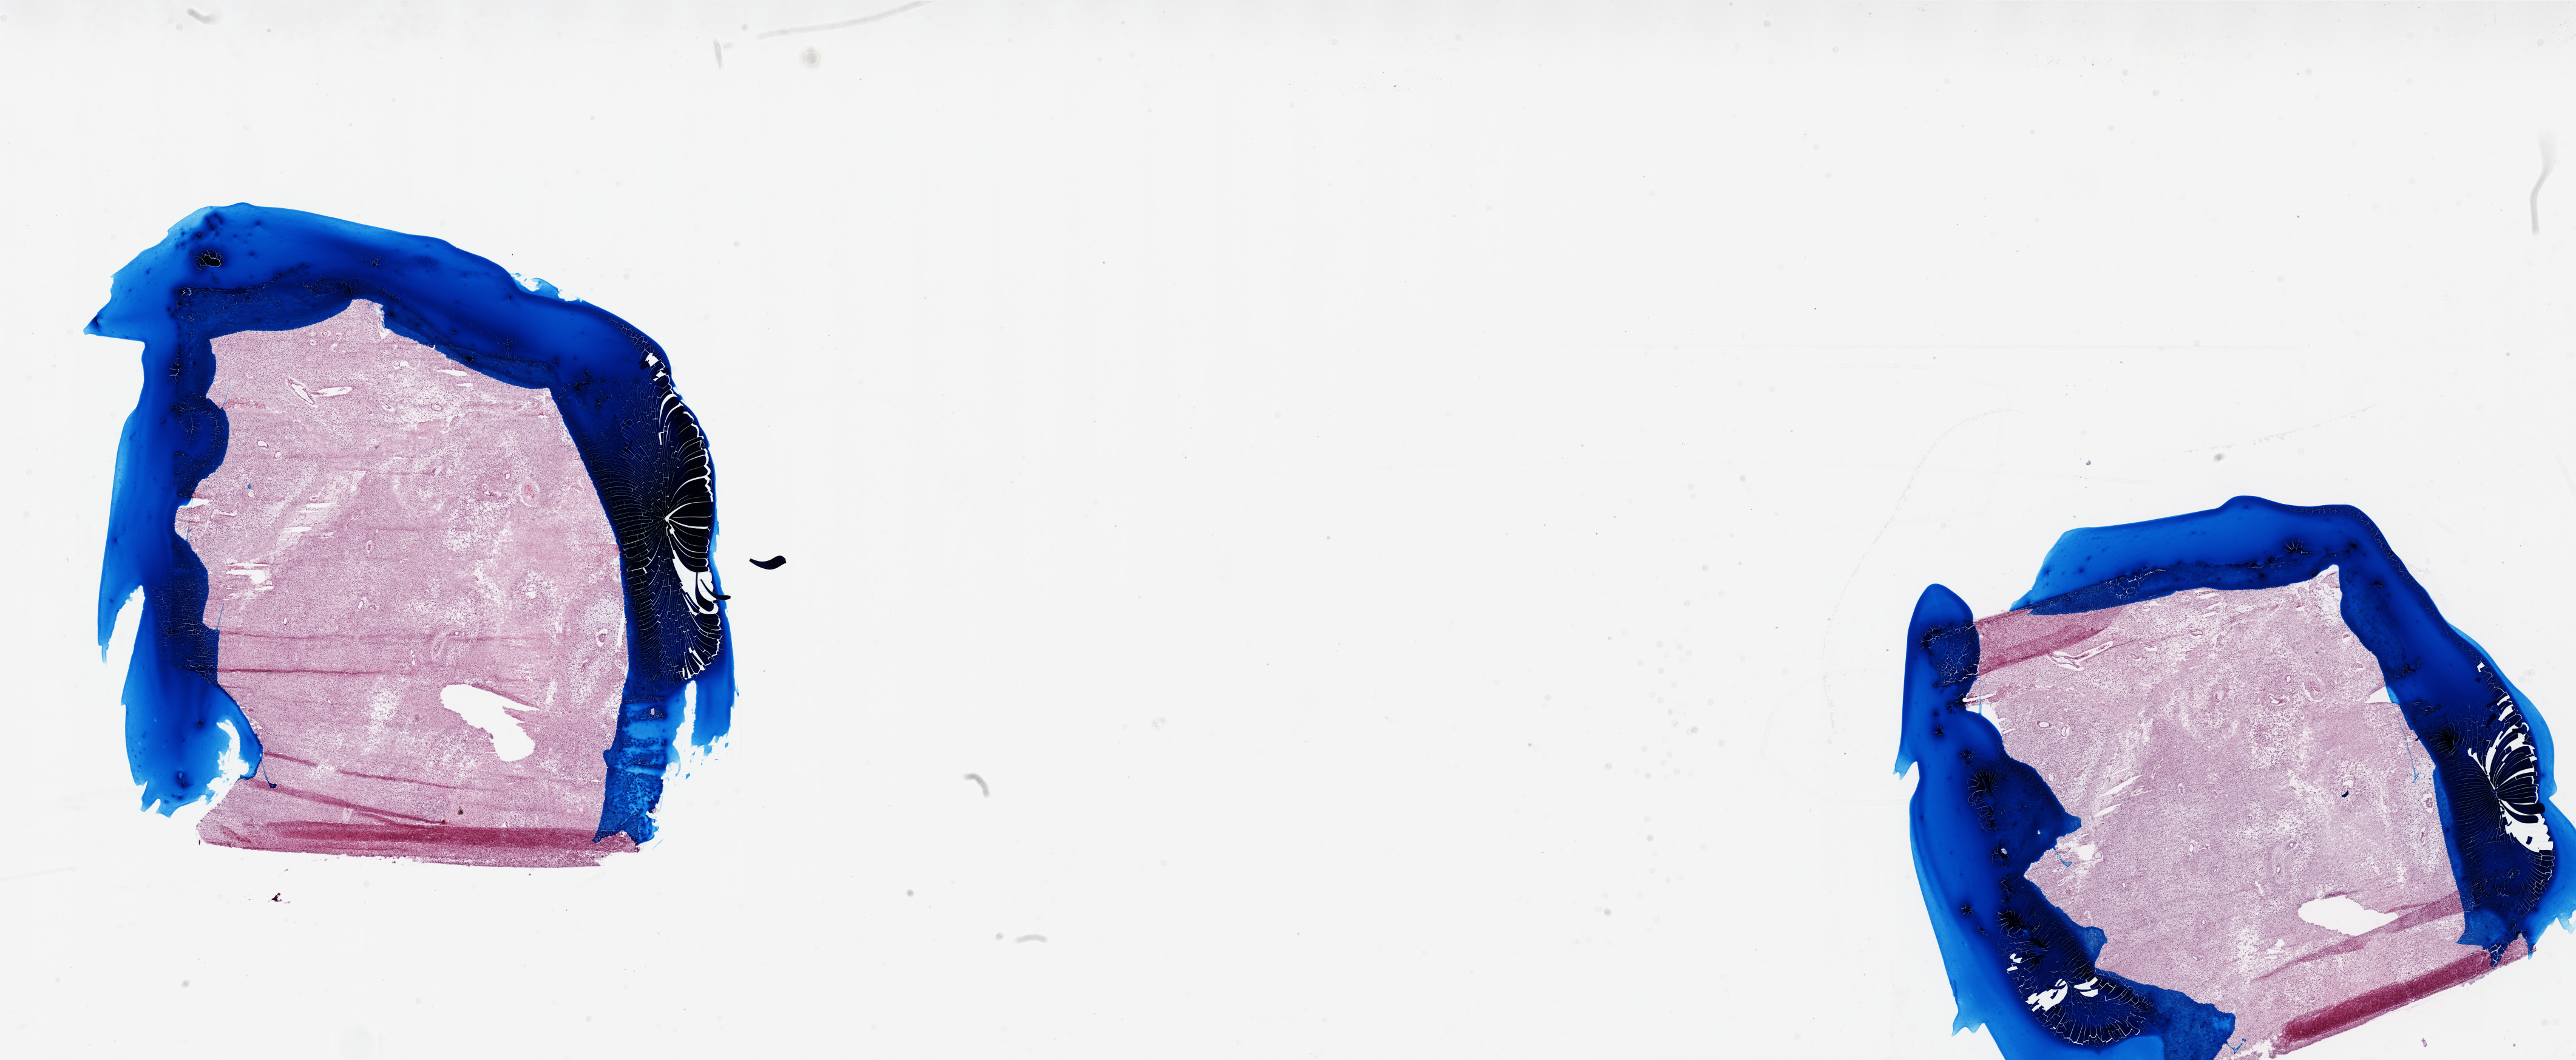
H&E whole-slide image, low-resolution overview of the scanned area, about 34.0 x 14.0 mm (slide scanned at 20x), frozen section, brain, primary tumour sample. Female, age 84 years at initial diagnosis. Slide review estimates, as recorded: tumour cells 80%, tumour nuclei 100%, normal cells 0%, stromal cells 0%, necrosis 20%.
Diagnosis: Glioblastoma.